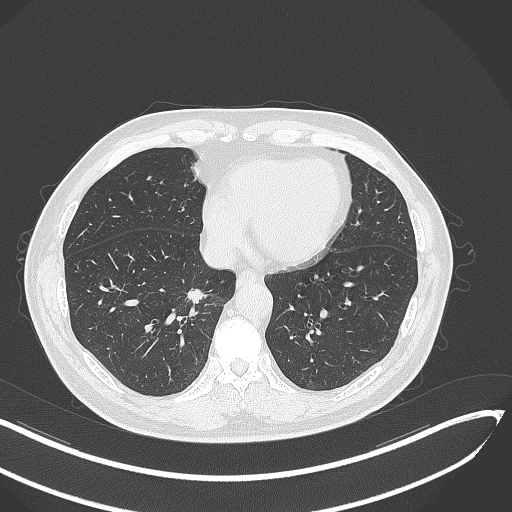
Chest CT, one axial slice. Slice 124 of 429 in the series (ordered by position). Reconstruction kernel B70f. Lung window (W 1500 / L -600 HU). 1 mm slice thickness. 512 × 512 image matrix, field of view 400 × 400 mm. Male patient, age 62 years. Case-level facts recorded for this patient, not image findings: clinical TNM (as recorded): T1b N0 M0; histopathological grade: G2.
Outlined on this slice (rectangle marked by the reading radiologist):
- lung tumour (recorded histology: adenocarcinoma): bounding box <182,287,213,315> (left, top, right, bottom; pixels)